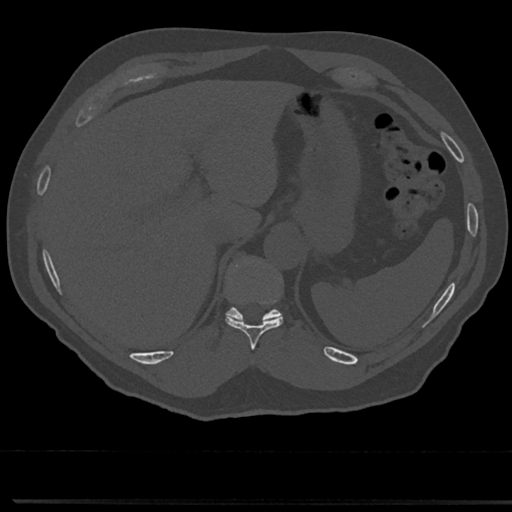
CT including the spine, one axial slice. Slice 239 of 817 in the series (ordered by position). Bone window (W 1800 / L 400 HU). 0.5 mm slice thickness. 512 × 512 image matrix, field of view 355 × 355 mm. Patient: male, 61 years. Case-level facts recorded for this patient, not image findings: primary cancer: prostate.
Outlined on this slice (semi-automatic segmentation, software-assisted and operator-edited):
- T10 vertebra: bounding box <226,261,283,348> (left, top, right, bottom; pixels)
- T11 vertebra: <227,261,280,321>